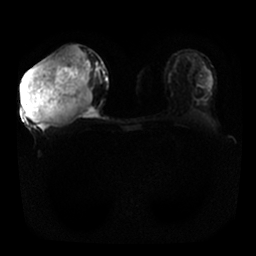
Breast MRI, one axial slice; slice 11 of 25 in the series (ordered by position); diffusion-weighted series; image 2 of 4 stored at this slice position (different b-values; order by instance number); 1.5 T; 256 × 256 image matrix, field of view 340 × 340 mm. Female patient.
Annotated regions visible in this slice (outlined manually by an expert reader):
- tumour on diffusion-weighted imaging: box from (x=21, y=44) to (x=93, y=125) px